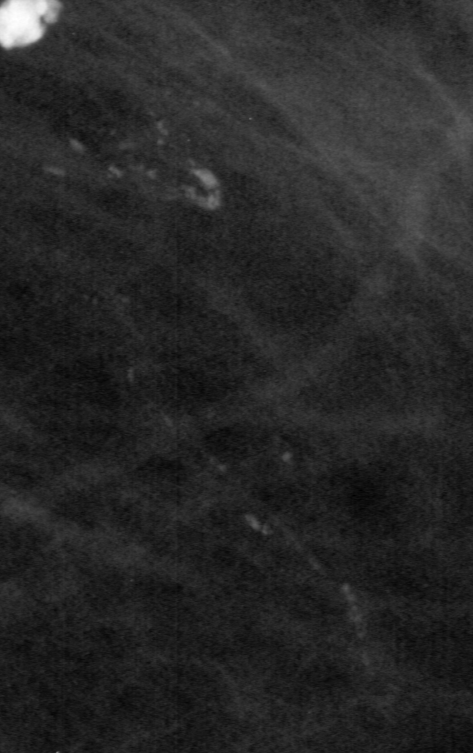
Cropped region of a digitized screen-film mammogram centred on a radiologist-marked abnormality; right breast; CC view.
Calcifications, morphology pleomorphic / fine linear branching, distribution linear; BI-RADS assessment category 5; pathology result (as recorded, not read from the image): malignant.